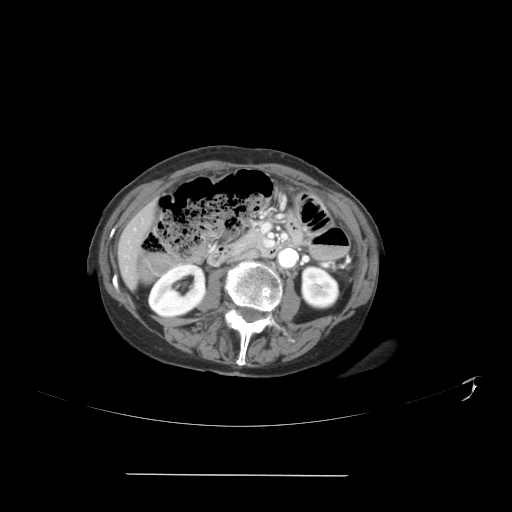
Contrast-enhanced abdominal CT, one axial slice; slice 12 of 41 in the series (ordered by position); reconstruction kernel STANDARD; soft-tissue window (W 400 / L 40 HU); 5 mm slice thickness; 512 × 512 image matrix, field of view 431 × 431 mm. Female patient, age 74 years. Case-level facts recorded for this patient, not image findings: diagnosis: colorectal cancer liver metastases, imaged before liver resection; multiple liver metastases: yes.
Structures marked on this image (outlined manually by an expert reader):
- liver: bounding box [x1, y1, x2, y2] px = [121, 208, 153, 284]
- planned liver remnant (the part of the liver to remain after resection): [125, 208, 153, 243]